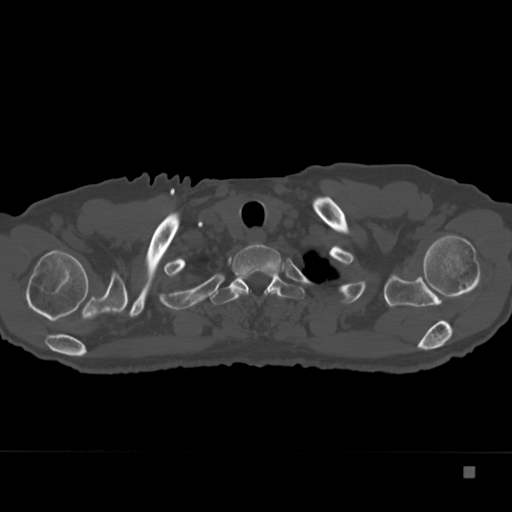
CT including the spine, one axial slice. Position 307 of 332 along the scan axis. Reconstruction kernel Br40s. Bone window (W 1800 / L 400 HU). 1.5 mm slice thickness. 512 × 512 image matrix. Male patient, age 72 years. From the clinical record (not read from this slice): primary cancer: skeletal.
Structures marked on this image (semi-automatic segmentation, software-assisted and operator-edited):
- T1 vertebra: bounding box [x1, y1, x2, y2] px = [230, 243, 282, 299]
- T2 vertebra: [210, 272, 305, 305]